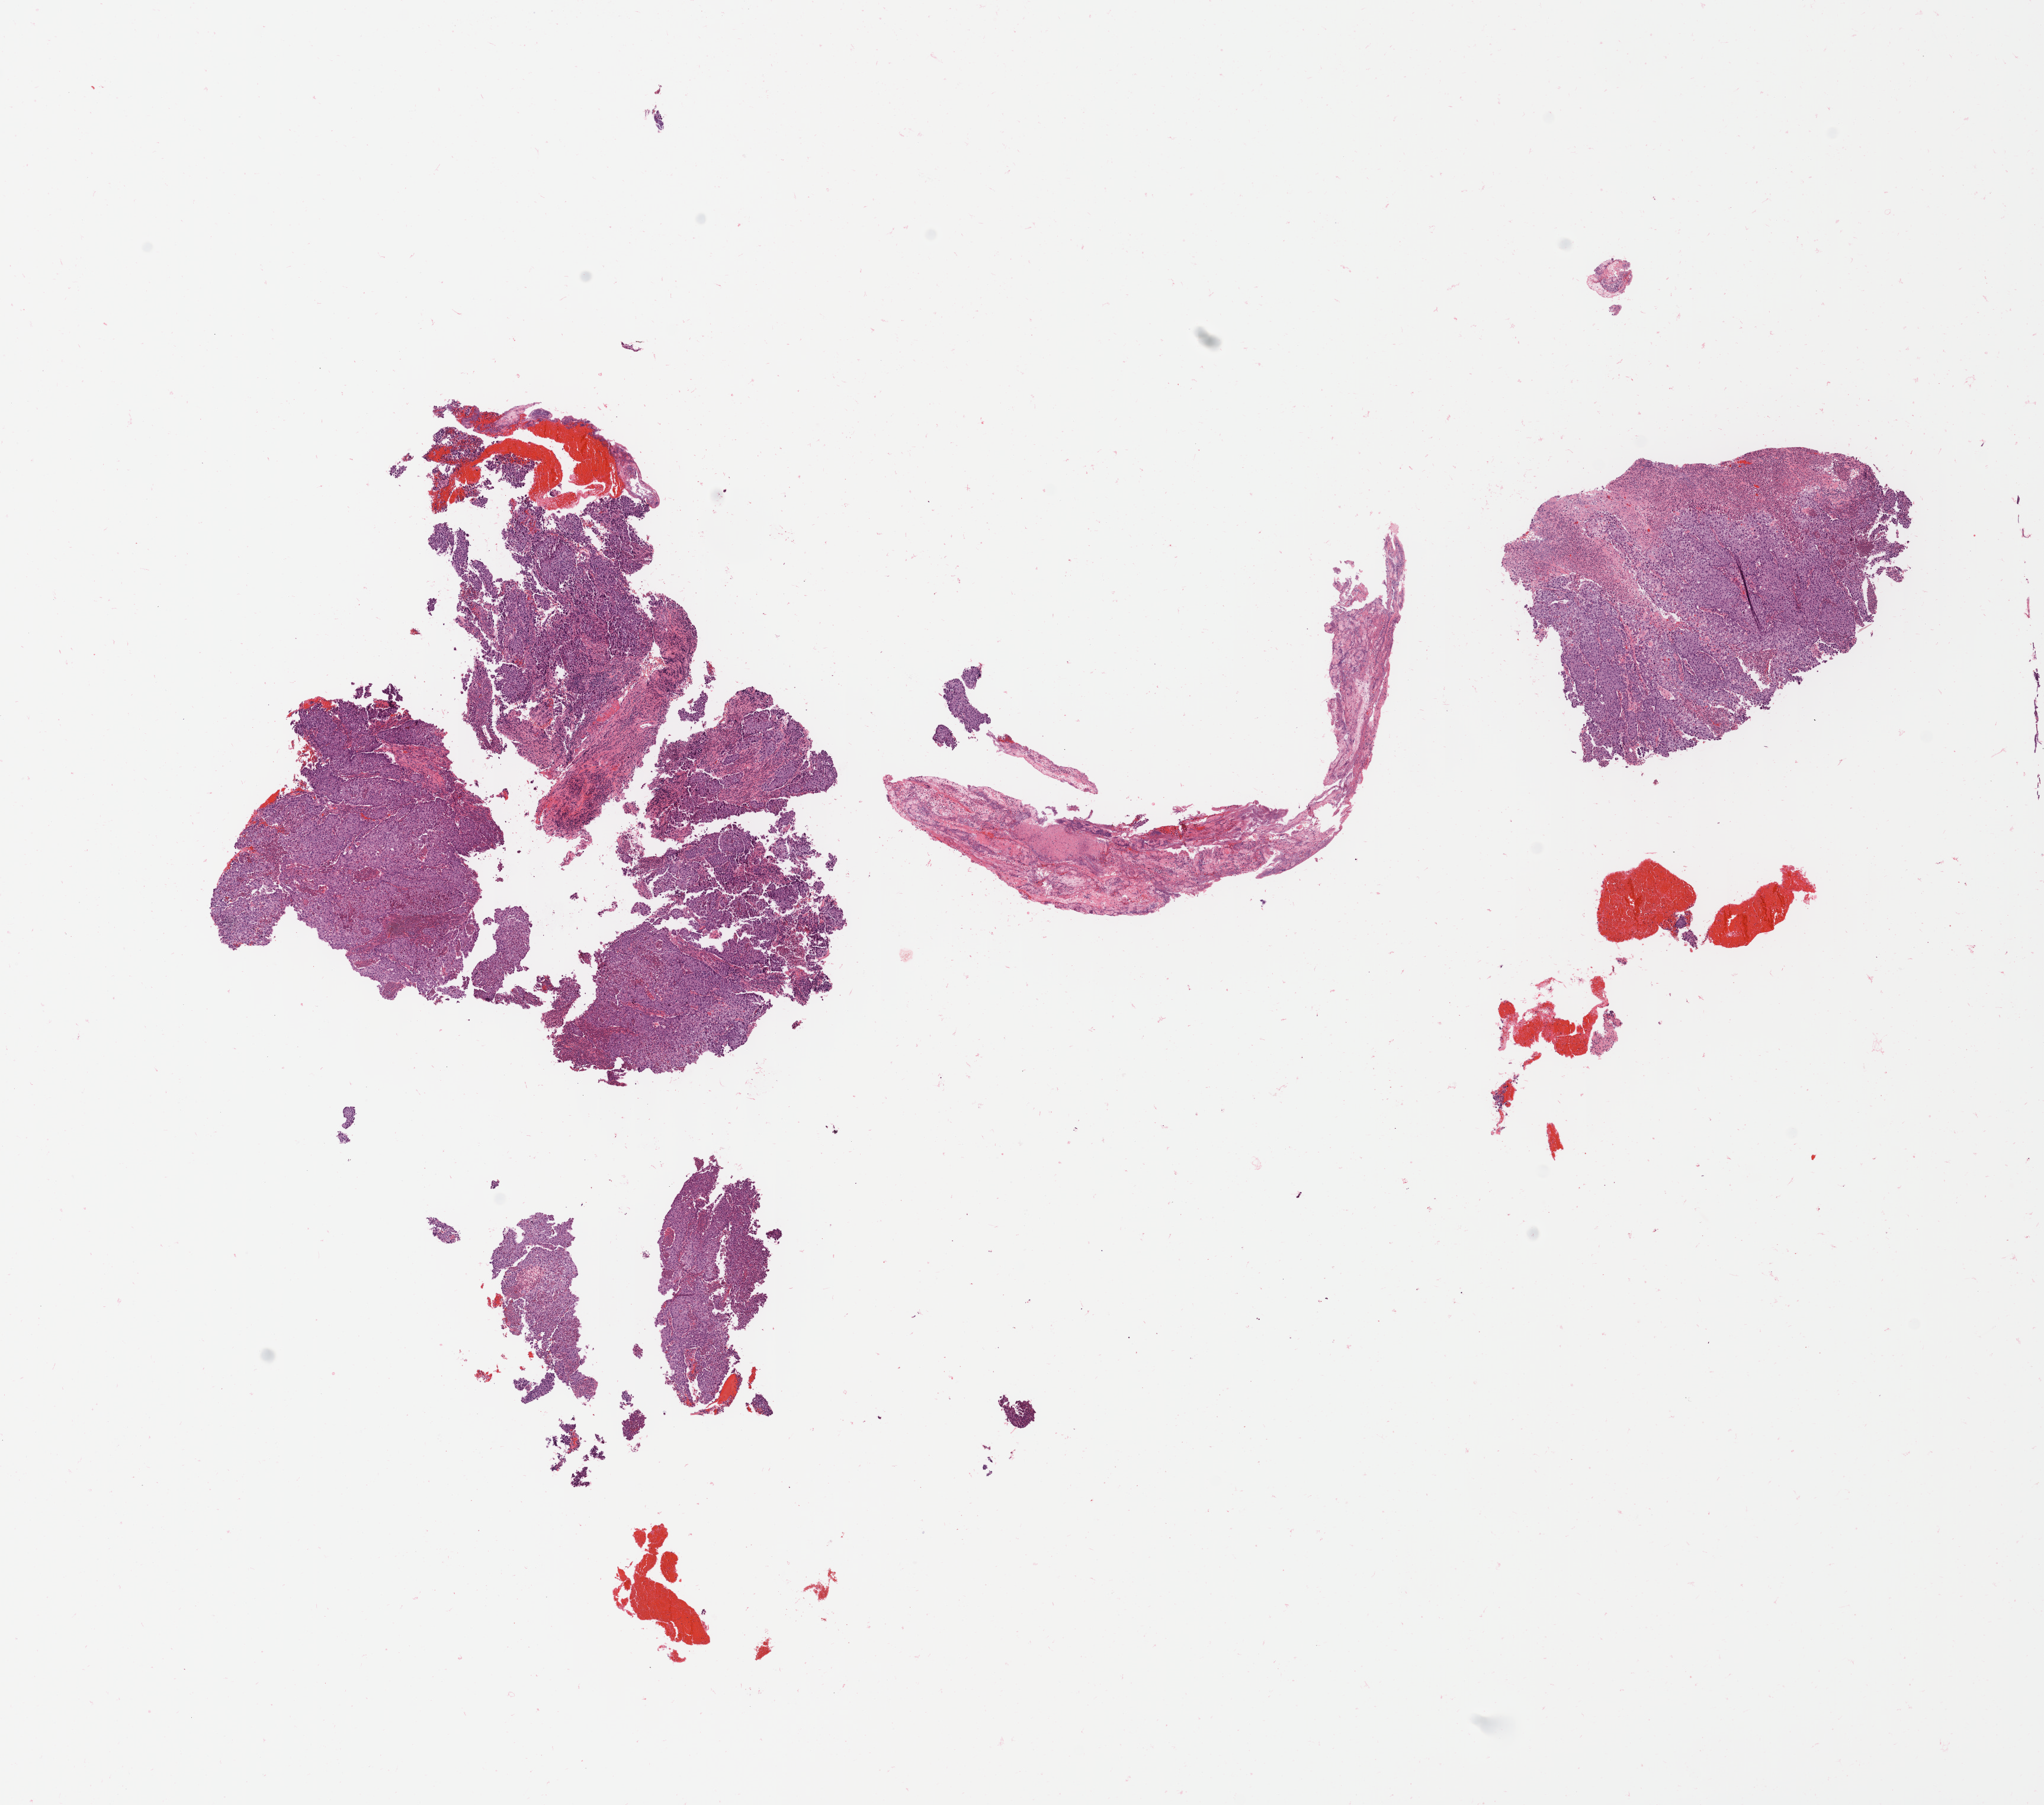
Hematoxylin and eosin (H&E) whole-slide image, shown as a low-resolution overview of the whole scanned area (about 13.7 x 12.1 mm). Tumor tissue. Site: cervix. Patient: female, 33 years old.
- diagnosis: Squamous cell carcinoma, large cell, nonkeratinizing, NOS